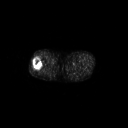
FDG PET of an extremity soft-tissue mass (from a PET/CT study), one axial slice. Position 238 of 267 along the scan axis. 3.27 mm slice thickness. 128 × 128 image matrix, field of view 700 × 700 mm. Patient: male, 43 years. From the clinical record (not read from this slice): histological type: poorly differentiated synovial sarcoma; grade: high; site of the primary tumour: right buttock.
Structures marked on this image (expert contour drawn on MRI and transferred to this co-registered scan by the dataset authors):
- gross tumour volume including surrounding oedema: box from (x=31, y=57) to (x=43, y=70) px
- gross tumour volume (mass): (x=33, y=58)–(x=43, y=70)